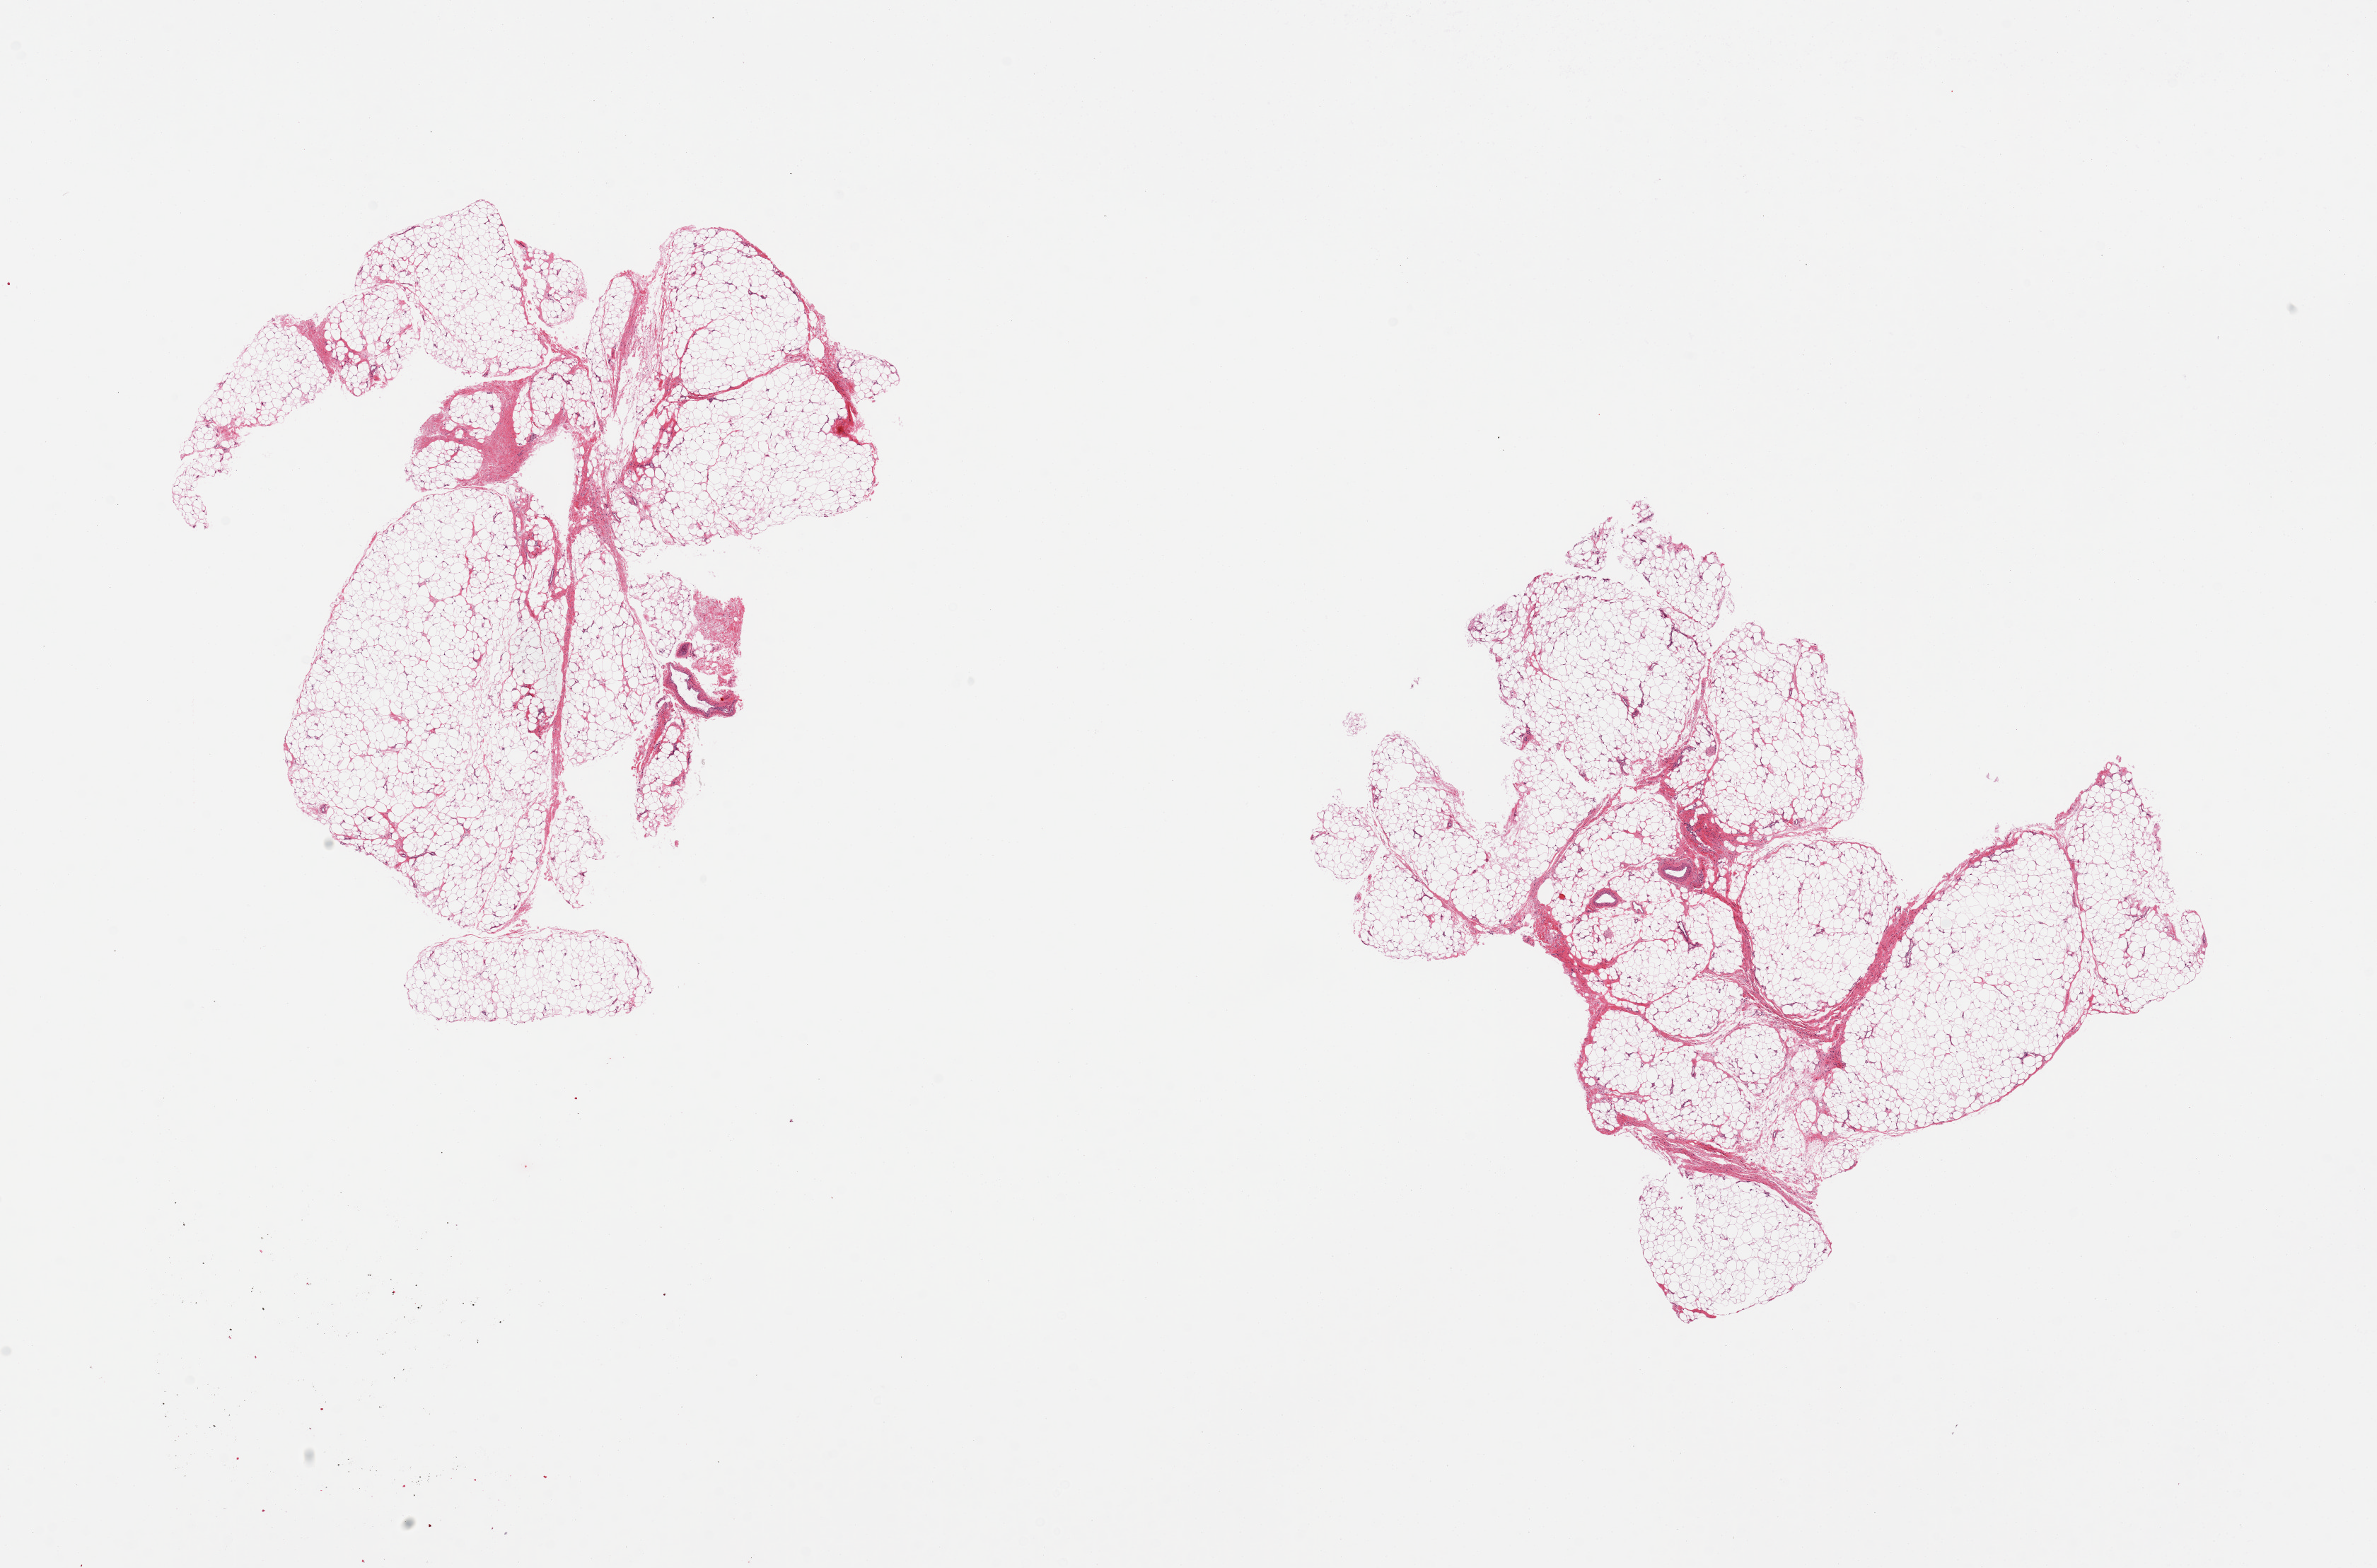
H&E whole-slide image, brightfield — shown as a low-resolution overview of the whole scanned area (about 26.6 x 17.5 mm, acquisition: 20x scan). PAXgene-fixed, paraffin-embedded tissue. Section of adipose tissue (target tissue). Tissue donor sample. Female donor.
Reviewer comment on this tissue sample: 2 pieces.